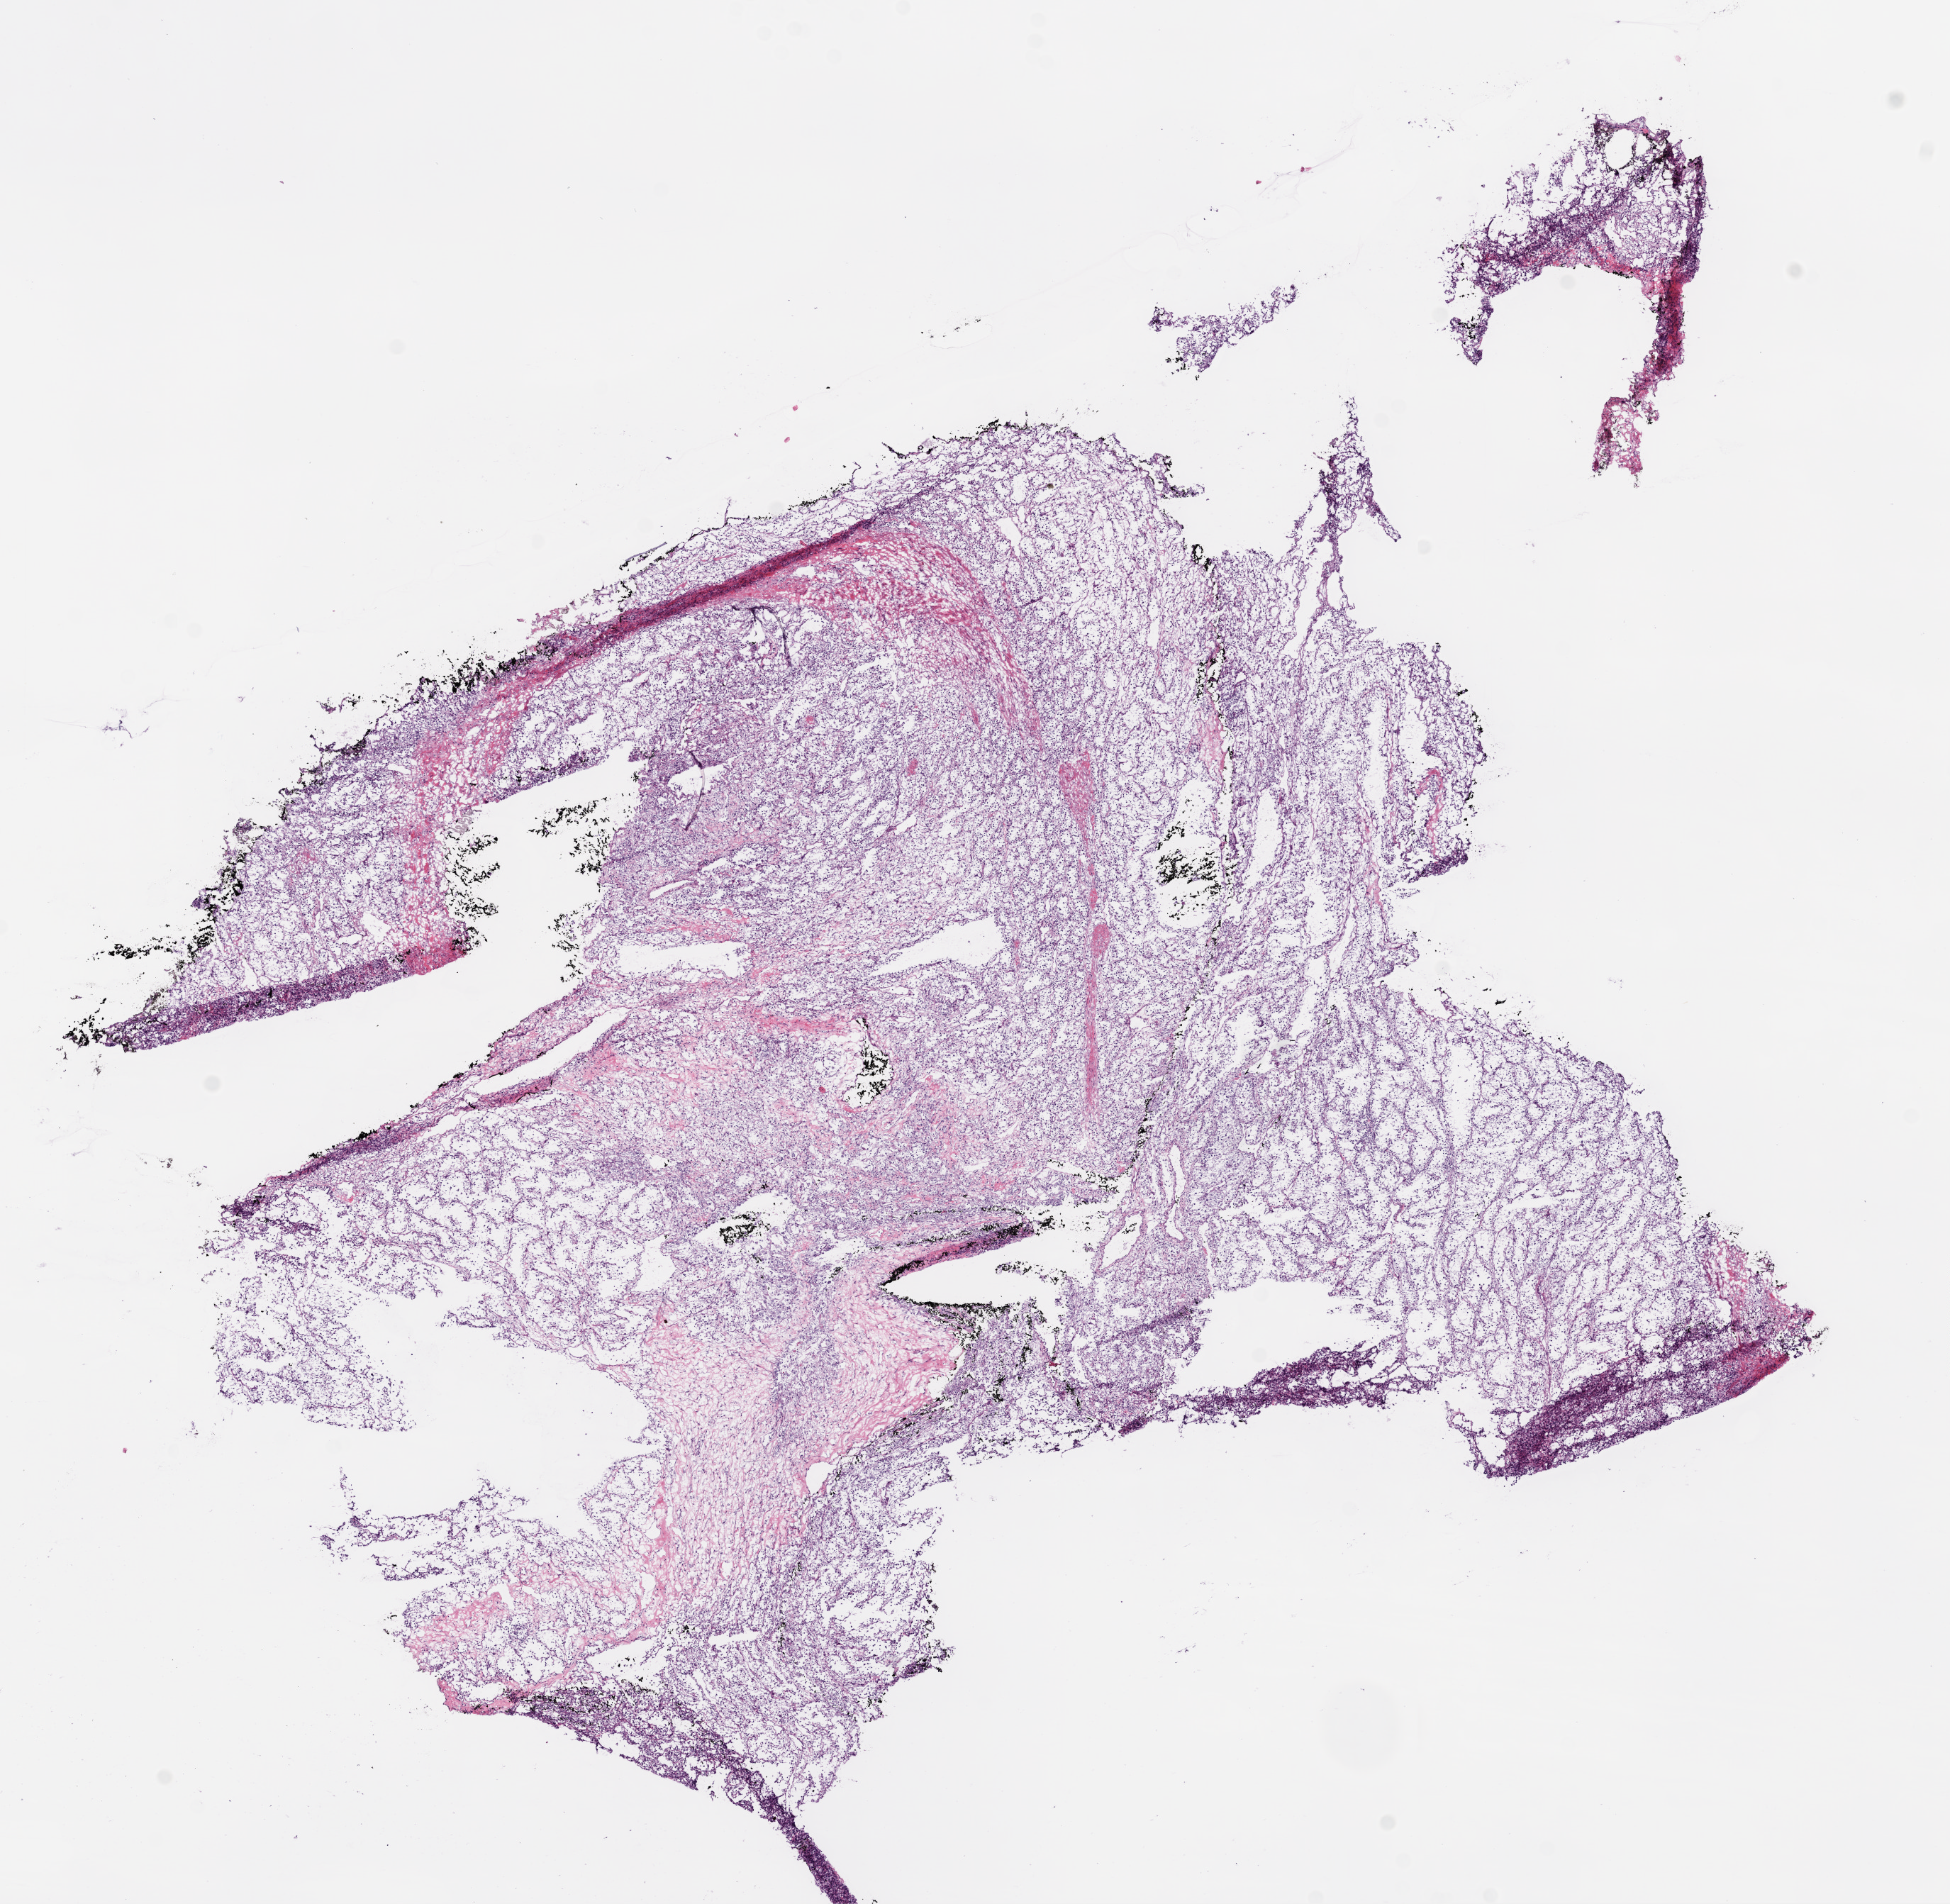
Hematoxylin and eosin (H&E) stained whole-slide image — a low-resolution overview of the entire scanned area, about 11.0 x 10.8 mm (from a 20x scan). Frozen section. Primary tumour sample from the kidney. Patient: female, age at initial diagnosis 77 years. Histologic grade: G2 (moderately differentiated). Composition of this section per pathologist review: tumour cells 90%, tumour nuclei 80%, normal cells 0%, stromal cells 10%, necrosis 0%.
AJCC pathologic stage: III. TNM: T3b N0 M0. Pathologic diagnosis: Clear cell adenocarcinoma, NOS.